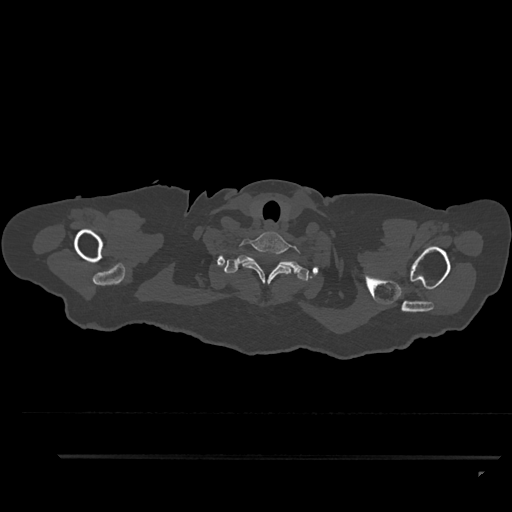
CT including the spine, one axial slice. Position 782 of 797 along the scan axis. Bone window (W 1800 / L 400 HU). 512 × 512 image matrix. Patient: female, 44 years. Case-level facts recorded for this patient, not image findings: primary cancer: renal; vertebrae with lytic lesions (as recorded): L1.
Outlined on this slice (semi-automatically segmented with operator editing):
- T1 vertebra: bounding box <223,255,309,281> (left, top, right, bottom; pixels)